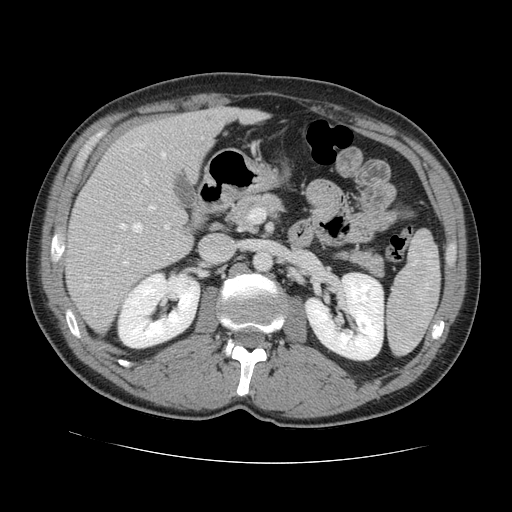
Contrast-enhanced abdominal CT, one axial slice; slice 68 of 131 in the series (ordered by position); intravenous contrast given; soft-tissue window (W 400 / L 40 HU); 512 × 512 image matrix, field of view 380 × 380 mm. Male patient, age 40 years. From the clinical record (not read from this slice): diagnosis: colorectal cancer liver metastases, imaged before liver resection; multiple liver metastases: yes; largest metastasis: 2.9 cm.
Structures marked on this image (expert manual segmentation):
- hepatic veins: bounding box (x1, y1, x2, y2) in pixels: (86, 143, 167, 286)
- liver: (67, 108, 262, 332)
- planned liver remnant (the part of the liver to remain after resection): (108, 108, 261, 187)
- portal vein (with intrahepatic branches): (123, 172, 169, 265)